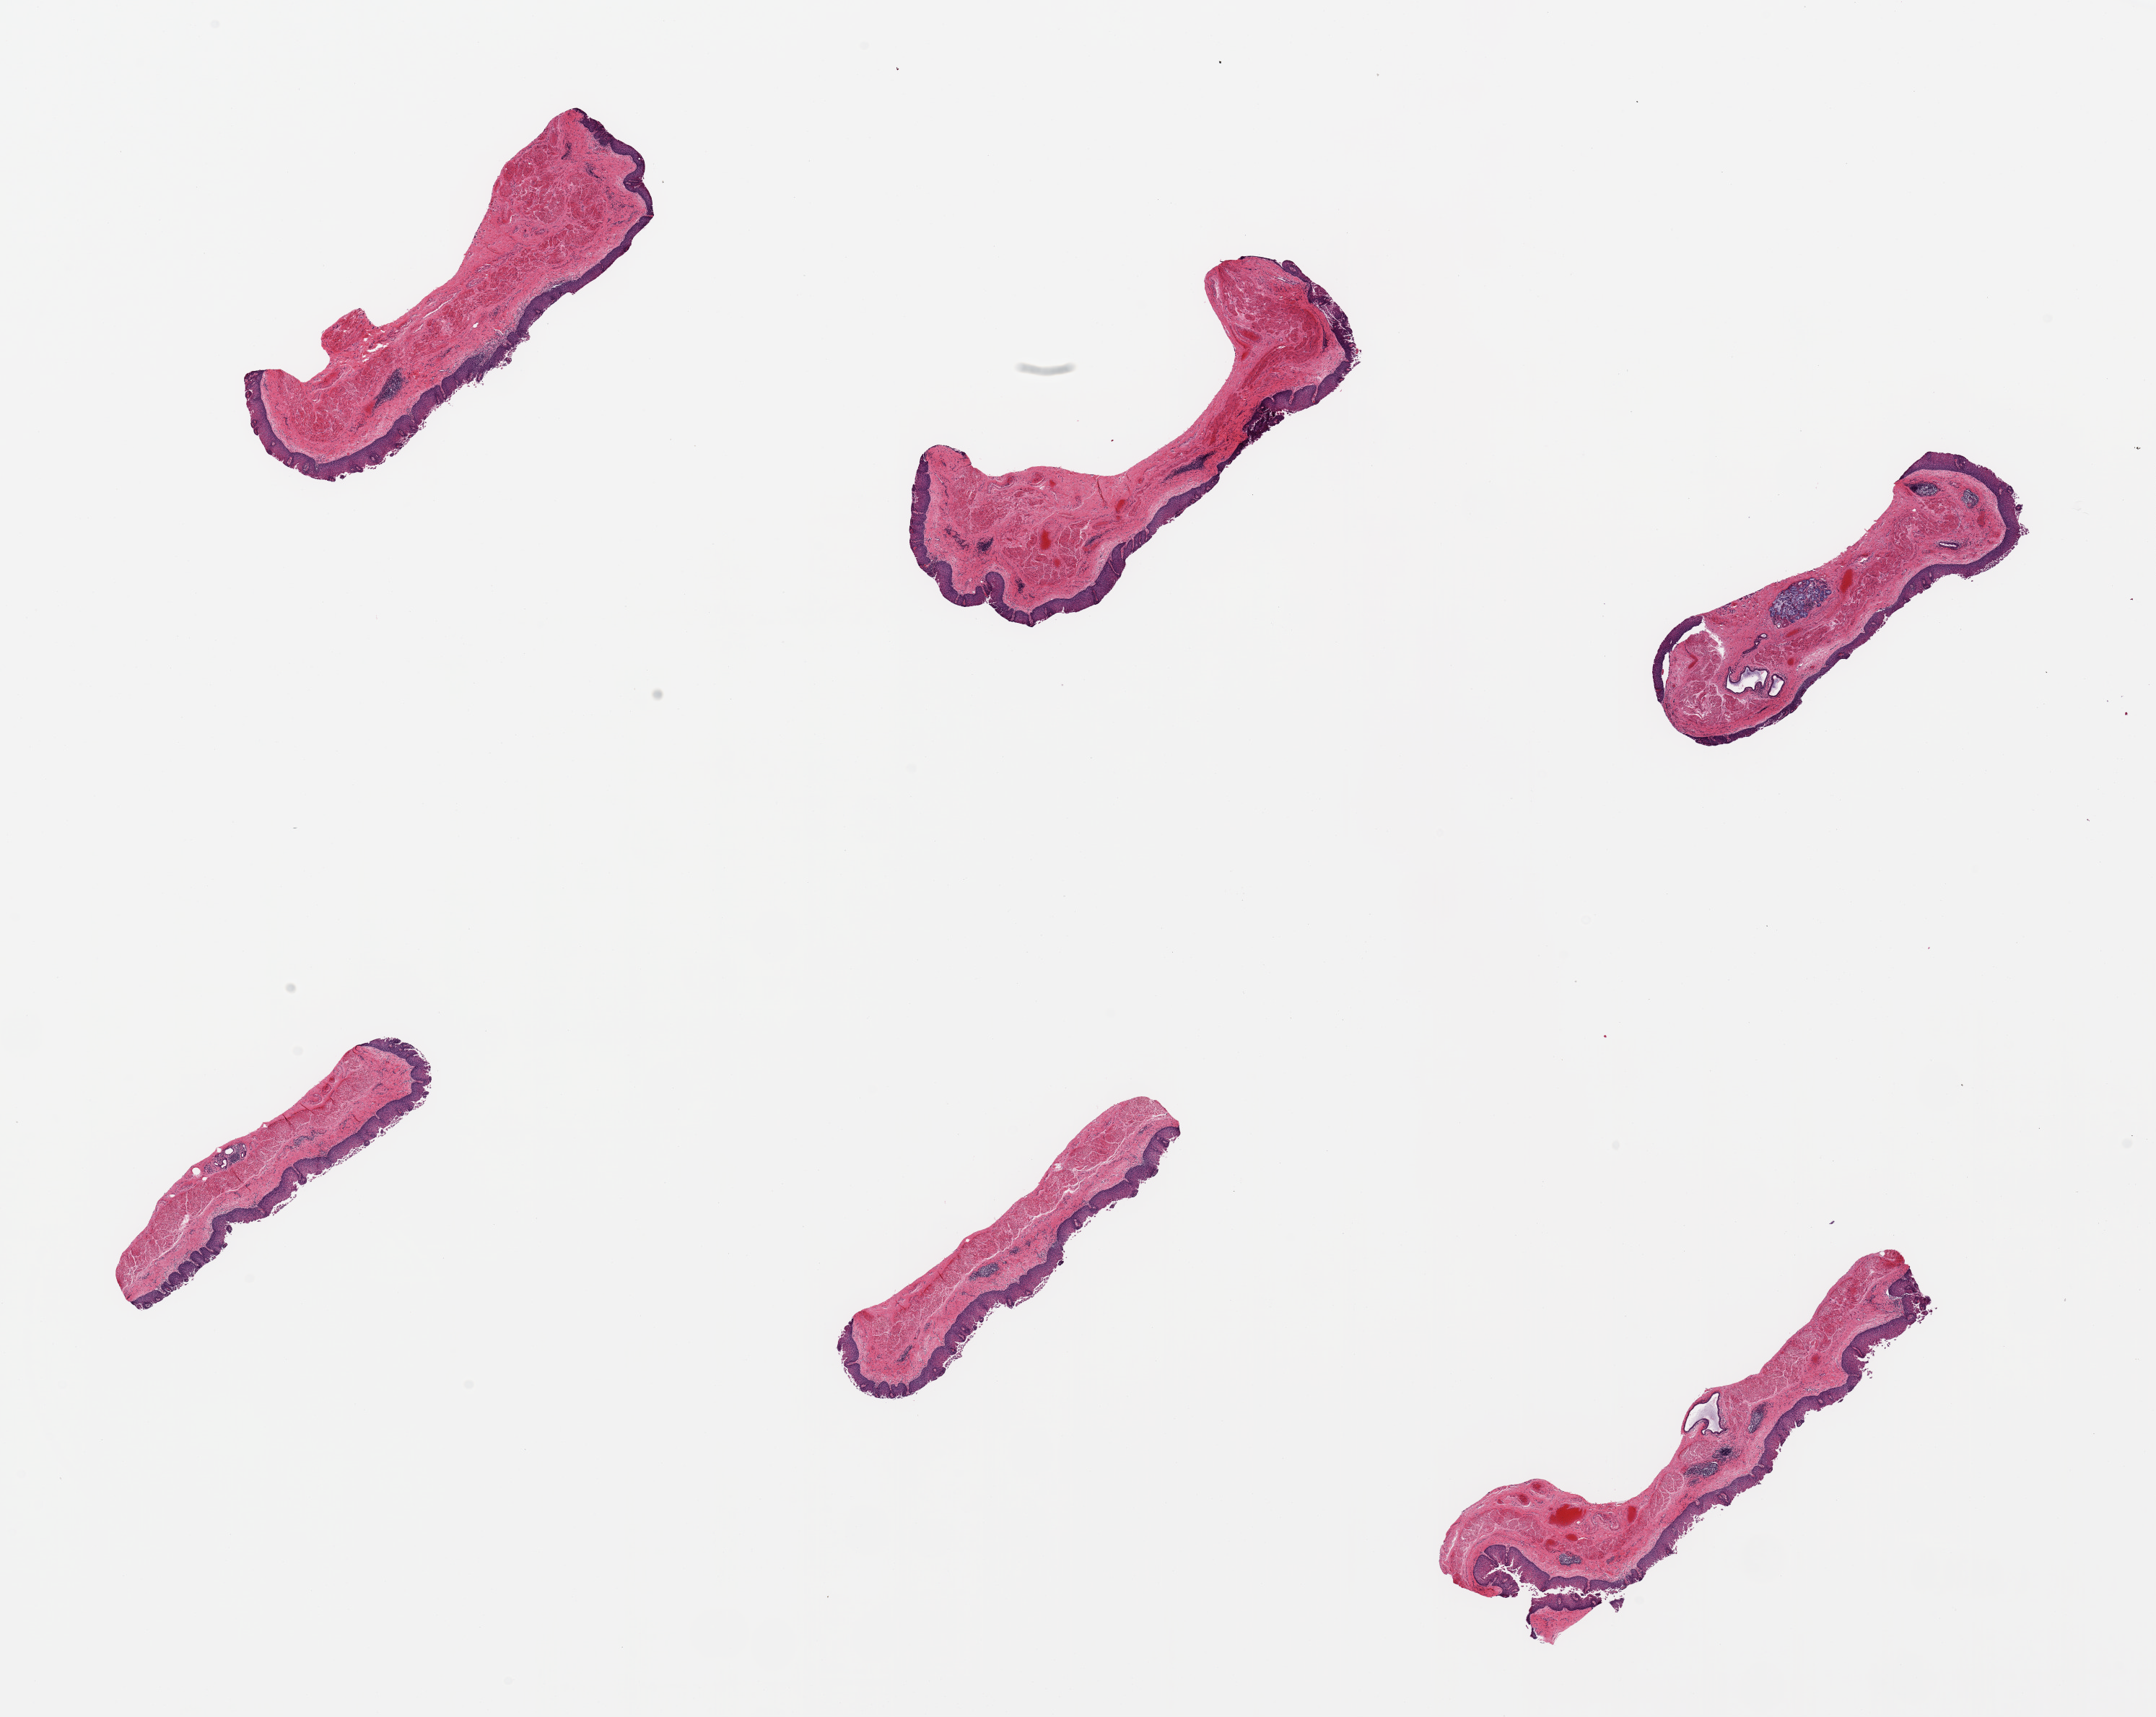
Haematoxylin and eosin whole-slide image, brightfield, a low-resolution overview of the entire scanned area, about 23.6 x 18.8 mm (slide scanned at 20x), PAXgene-fixed, paraffin-embedded tissue, section of esophageal mucous membrane (target tissue), donor tissue sample. Donor sex: male.
Pathologist's review note for this sample: 6 pieces; partially sloughed epithelium; foci of chronic esophagitis.